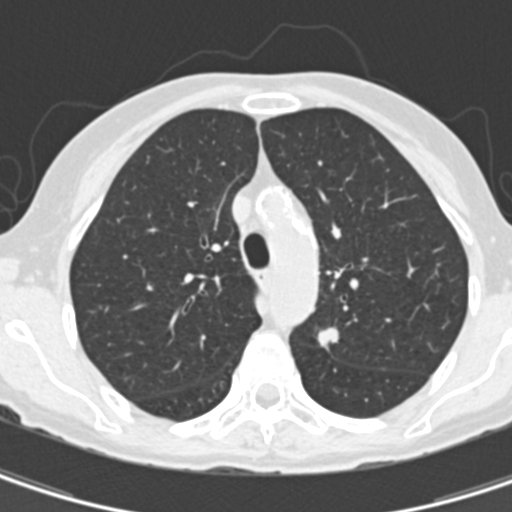
Low-dose screening chest CT, one axial slice. Position 111 of 157 along the scan axis. Reconstruction kernel B30f. 120 kVp. Lung window (W 1500 / L -600 HU). 512 × 512 image matrix.
Annotated regions visible in this slice (expert manual segmentation):
- lesion 1 (tumor, upper lobe of left lung): bounding box <317,327,339,350> (left, top, right, bottom; pixels)